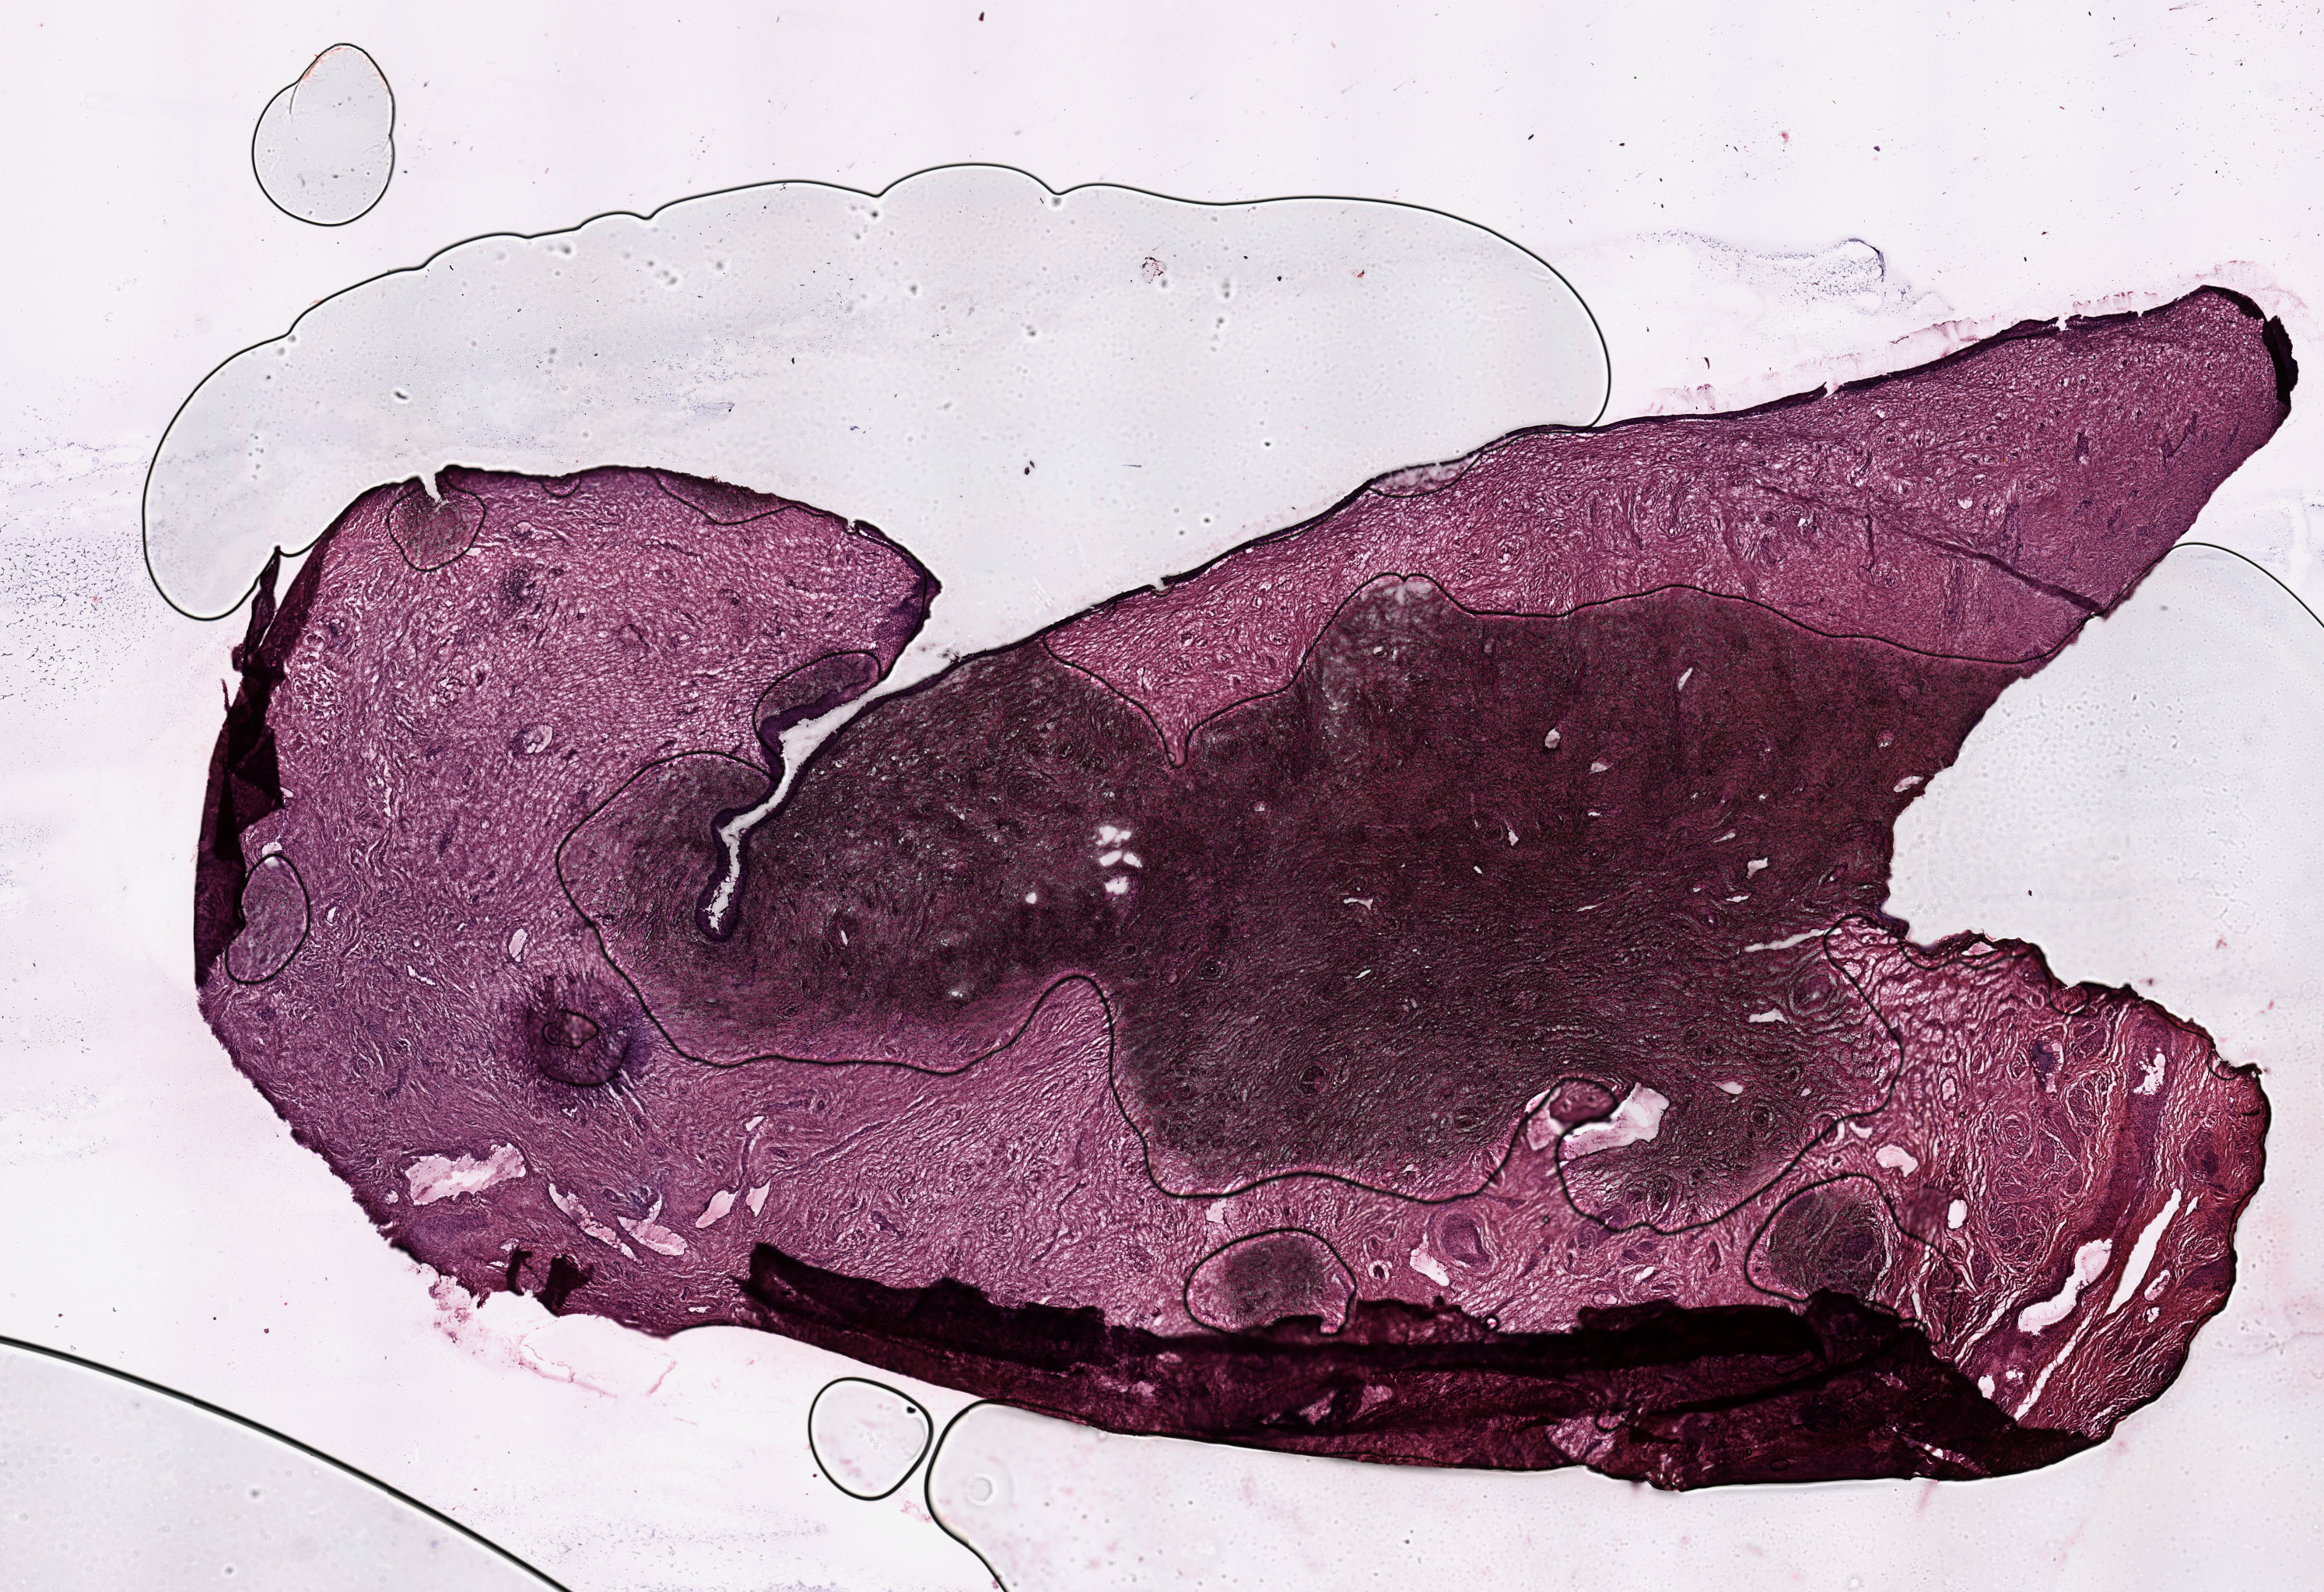
H&E whole-slide image, whole scanned area (about 11.8 x 8.1 mm) shown as a low-resolution overview; uterus, normal (non-tumour) tissue. Female, 66 y/o.
• this section: normal (non-tumour) tissue from the same patient
• patient diagnosis: Endometrioid adenocarcinoma, NOS